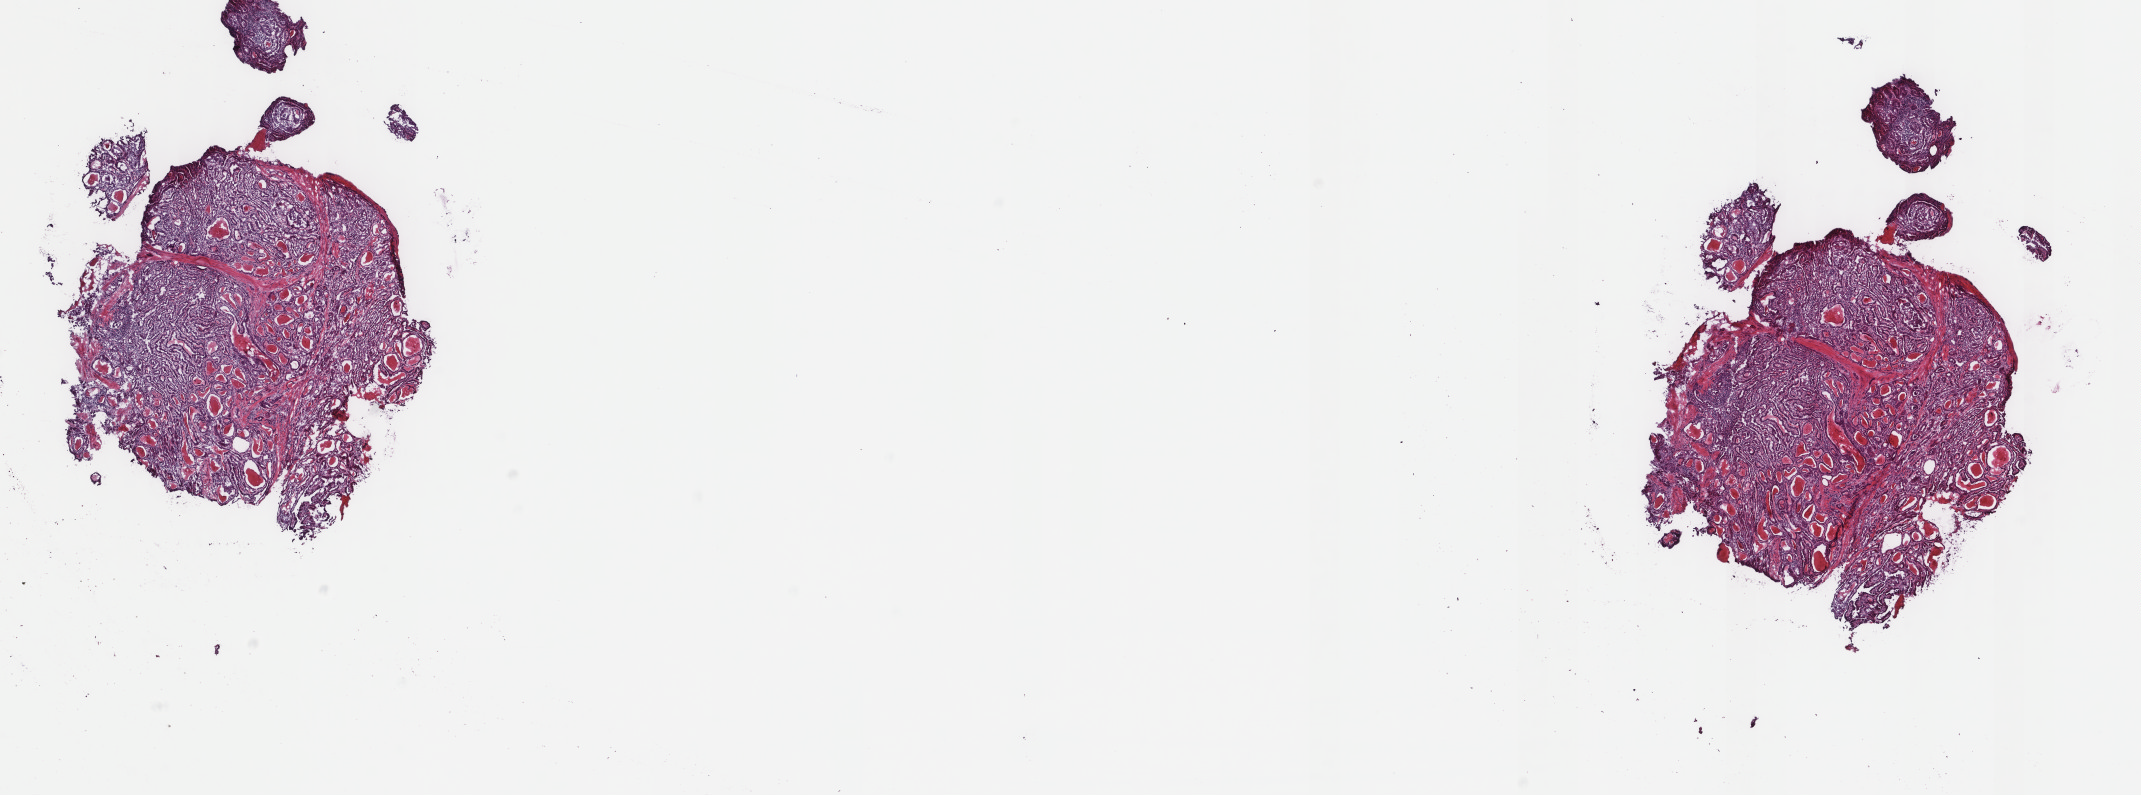
Whole-slide histology image, H&E-stained, low-resolution overview of the scanned area, about 17.0 x 6.3 mm, frozen section, thyroid, primary tumour sample. Female, age 53 years at initial diagnosis. Composition of this section per pathologist review: tumour cells 100%, tumour nuclei 80%.
Pathologic diagnosis: Papillary adenocarcinoma, NOS (thyroid gland).